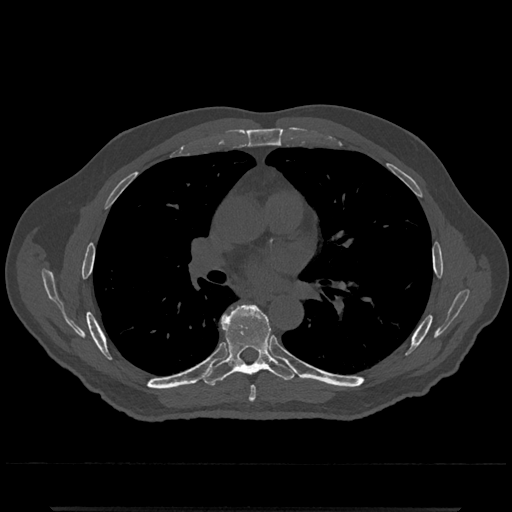
CT including the spine, one axial slice; position 736 of 797 along the scan axis; bone window (W 1800 / L 400 HU); 512 × 512 image matrix. Patient: male, 67 years. Case-level facts recorded for this patient, not image findings: primary cancer: prostate.
Annotated regions visible in this slice (semi-automatic segmentation, software-assisted and operator-edited):
- T6 vertebra: box from (x=228, y=314) to (x=256, y=402) px
- T7 vertebra: (x=203, y=304)–(x=296, y=386)